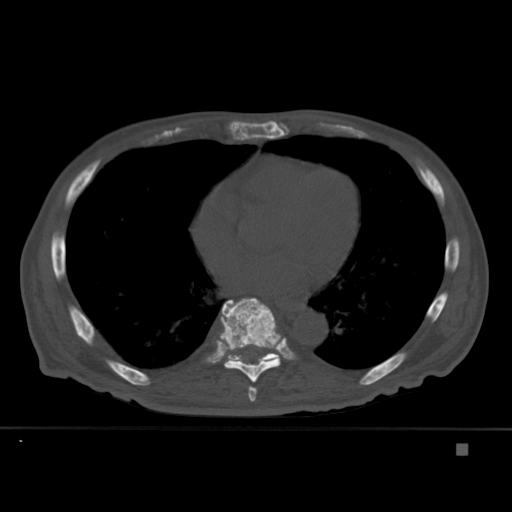
CT including the spine, one axial slice; position 260 of 451 along the scan axis; bone window (W 1800 / L 400 HU); 512 × 512 image matrix. Male patient, age 75 years. Case-level facts recorded for this patient, not image findings: primary cancer: prostate.
Structures marked on this image (semi-automatically segmented with operator editing):
- T7 vertebra: bounding box [x1, y1, x2, y2] px = [248, 386, 257, 402]
- T8 vertebra: [220, 298, 281, 383]
- T9 vertebra: [224, 347, 279, 364]